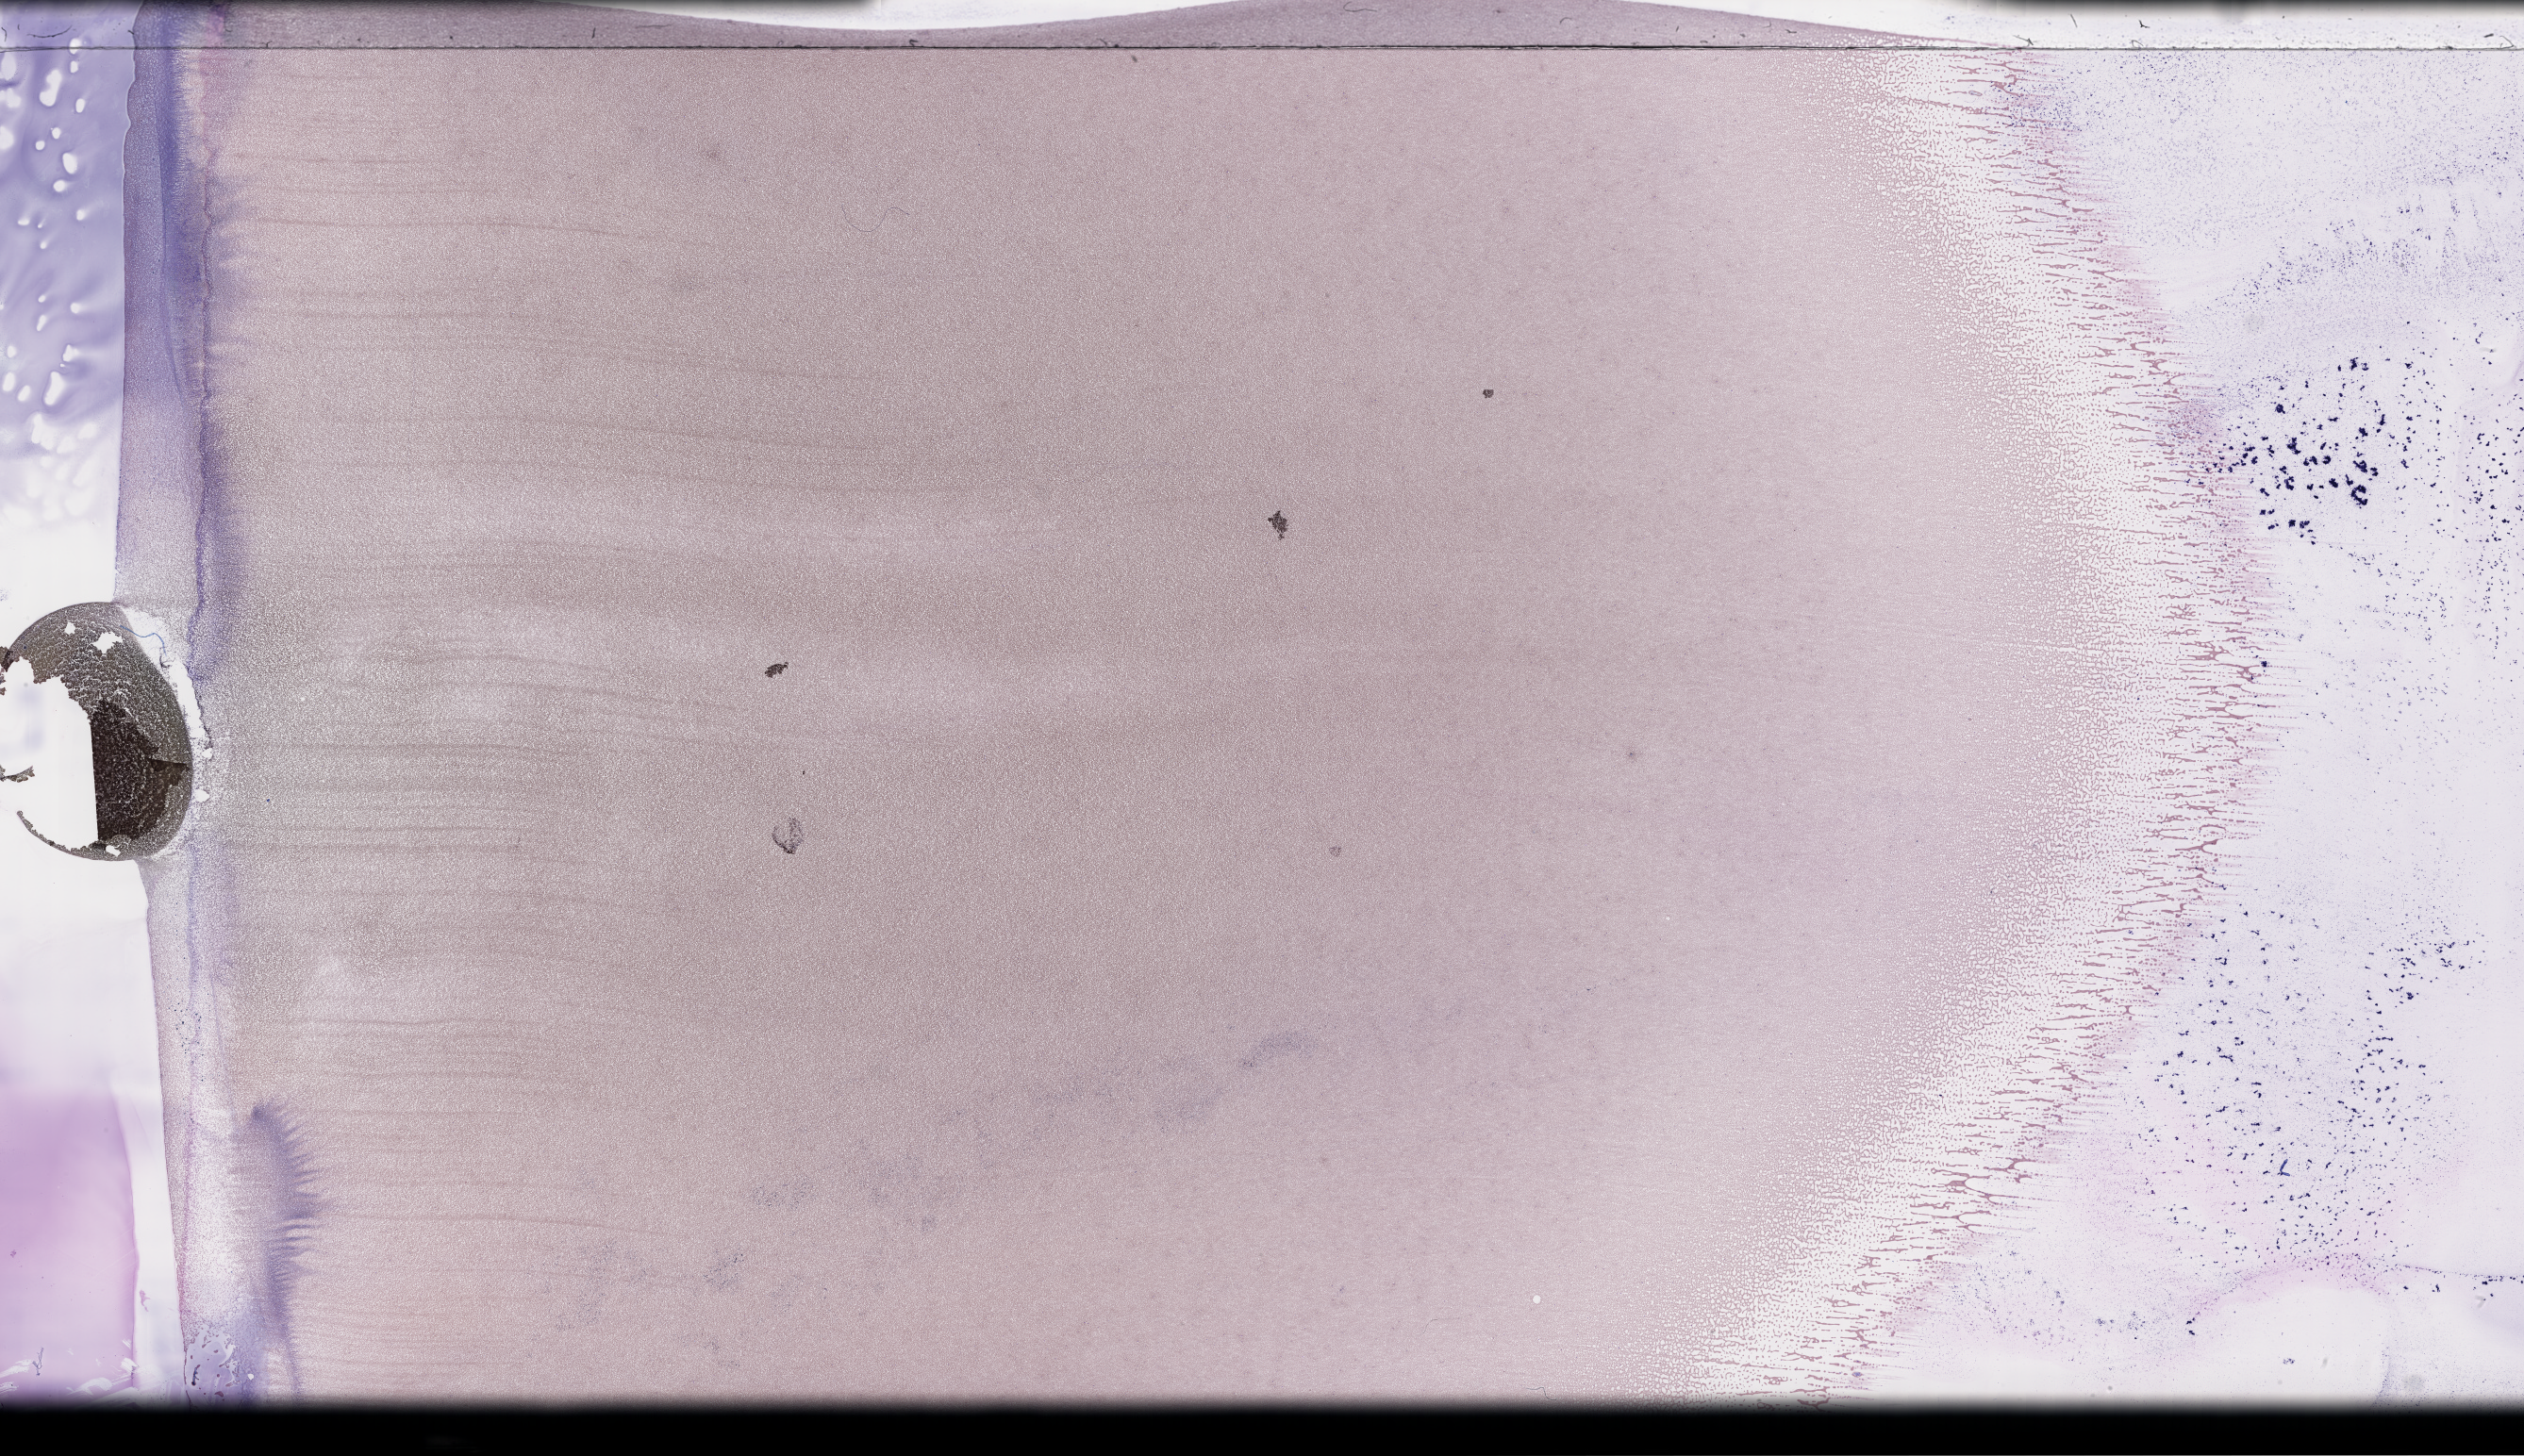
Wright–Giemsa-stained whole blood smear, whole-slide image — low-resolution overview of the scanned area, about 43.2 x 24.9 mm; specimen time point: collected on treatment. Patient: male.
Patient diagnosis: Plasma Cell Myeloma.